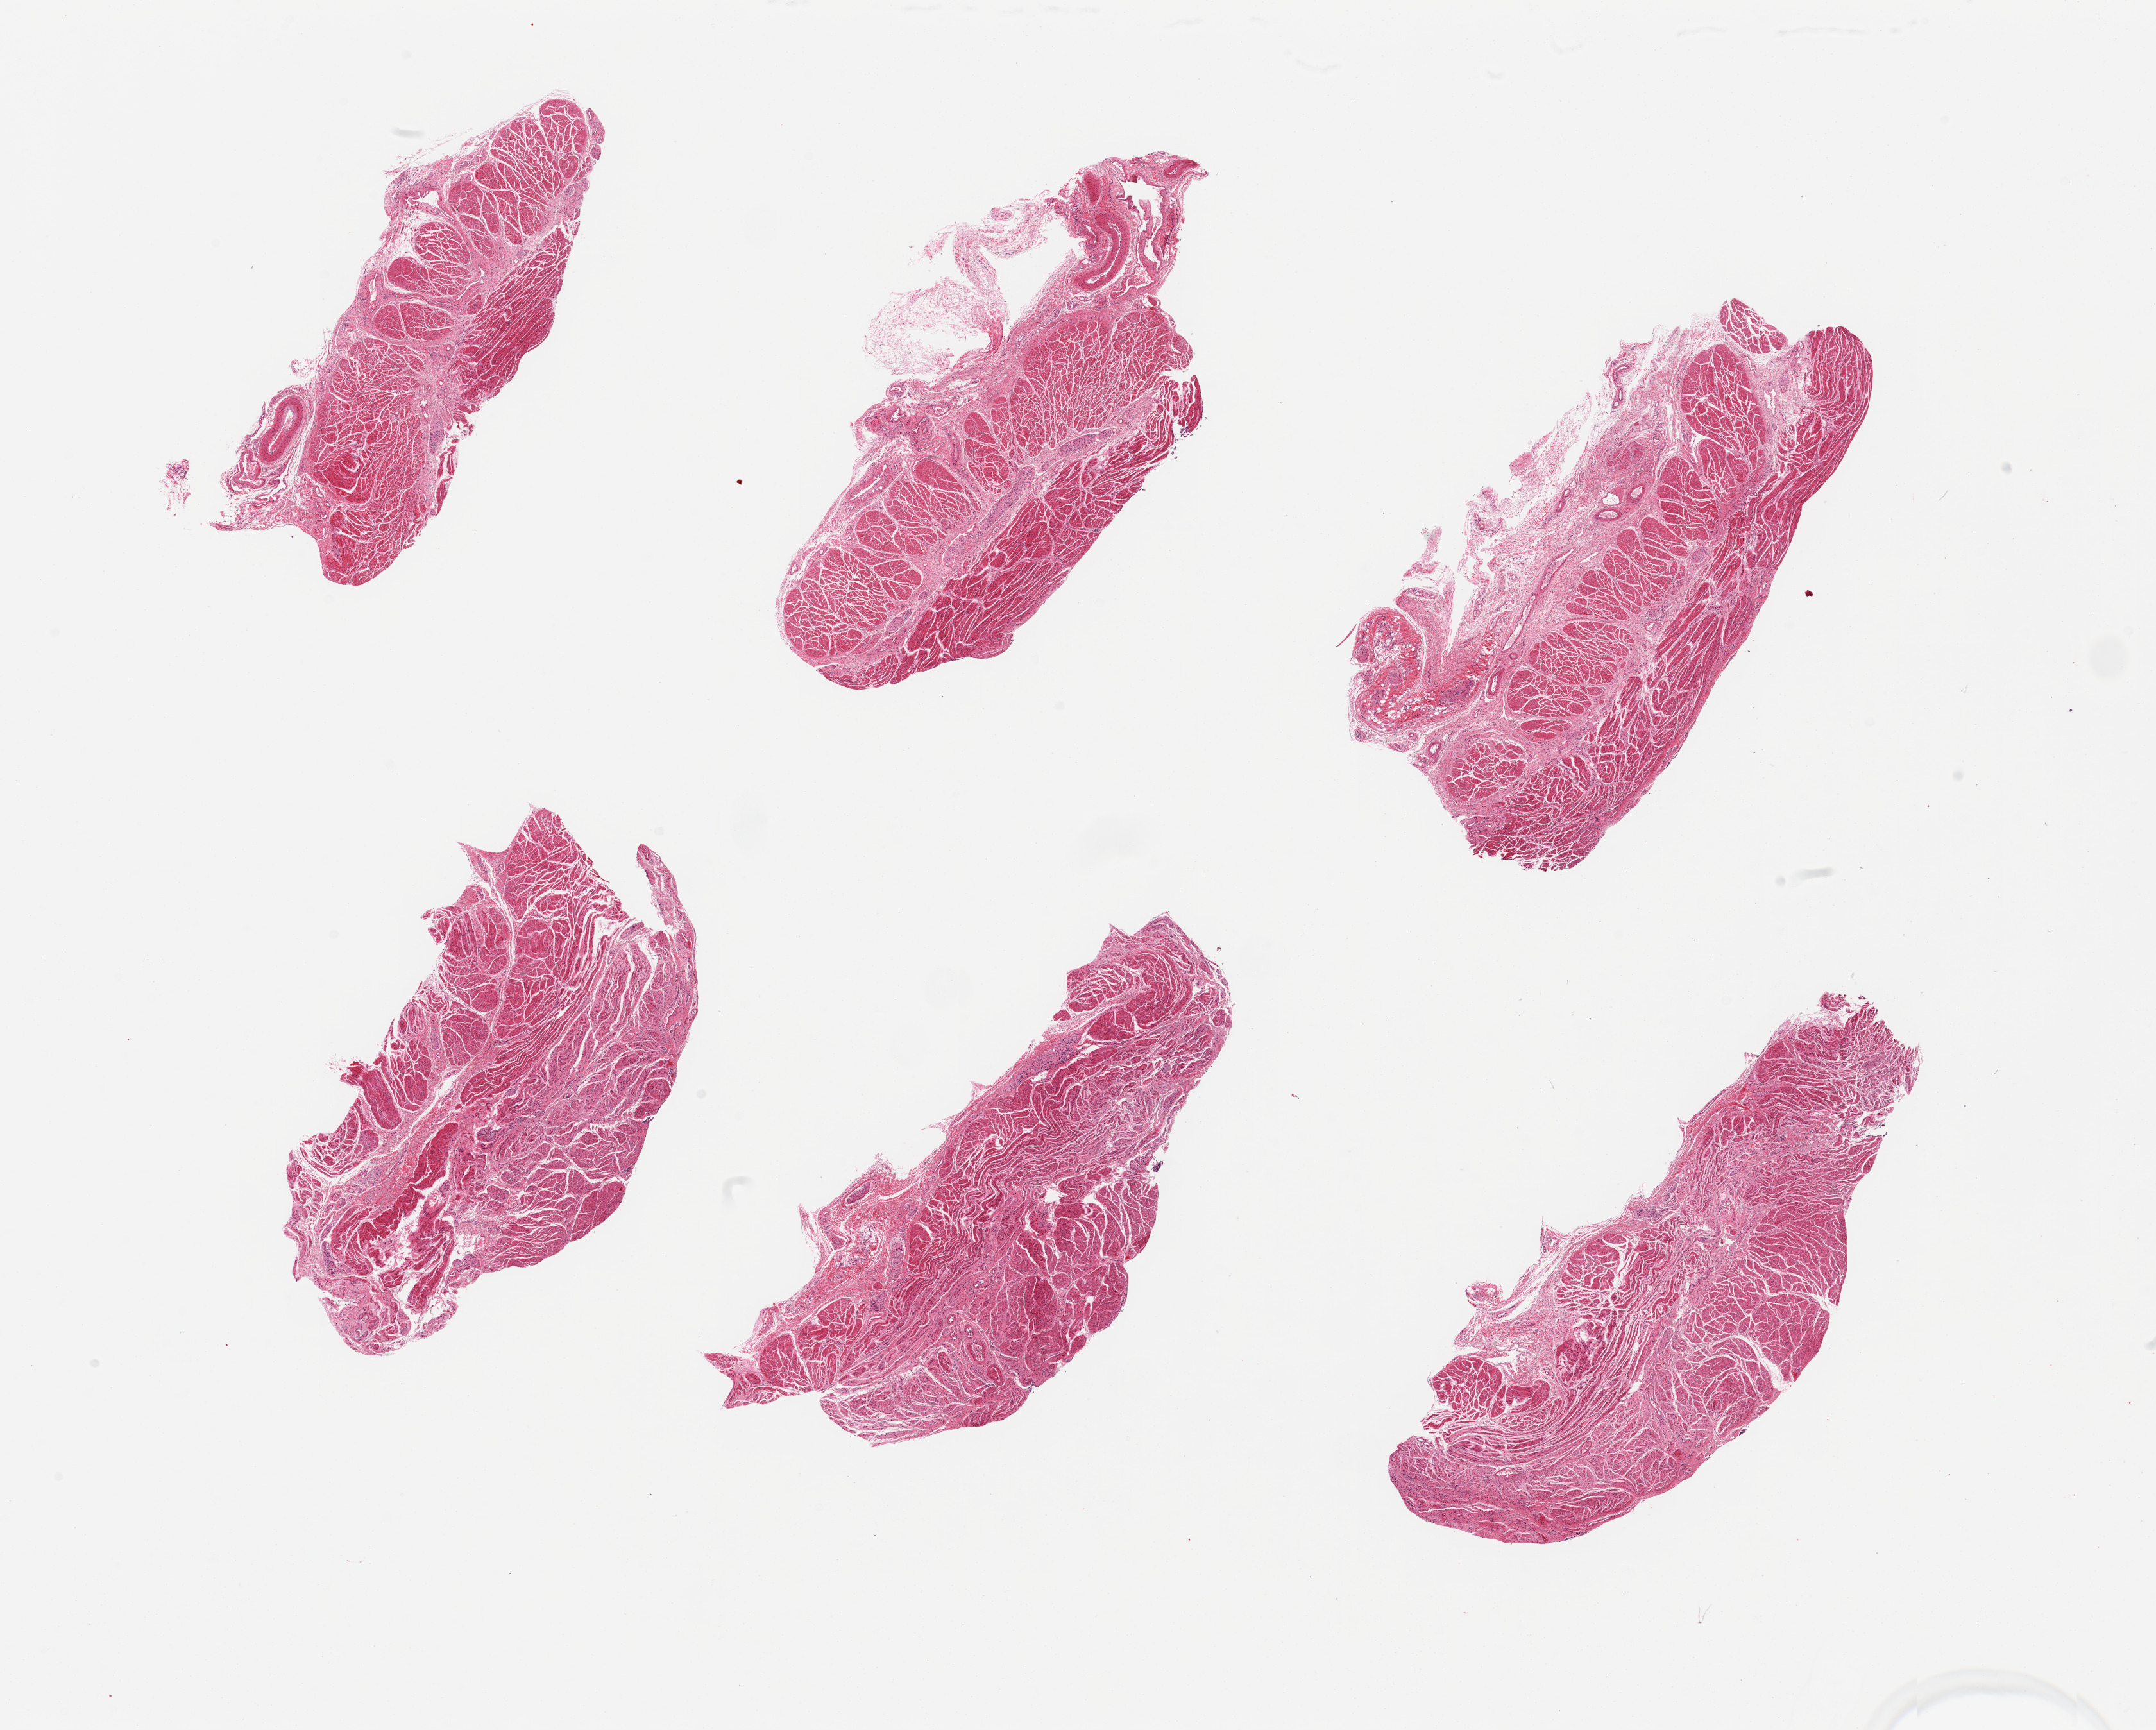
Whole-slide image, H&E stain — low-resolution overview of the scanned area, about 26.6 x 21.3 mm, PAXgene-fixed, paraffin-embedded tissue, sampled site (target tissue): gastroesophageal junction, tissue donor sample. Donor: male.
* review note (as recorded): 6 pieces, all muscularis, good specimens